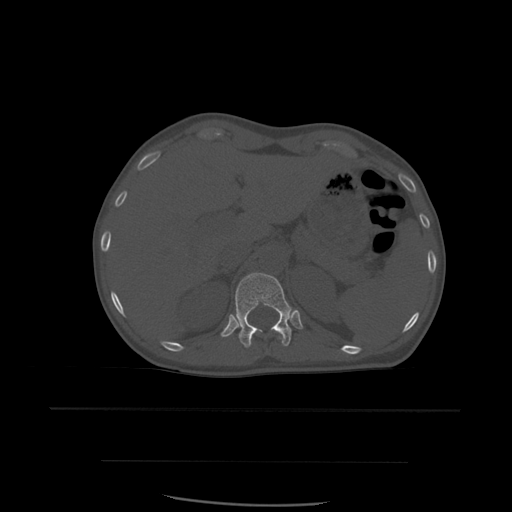
CT including the spine, one axial slice; position 277 of 574 along the scan axis; bone window (W 1800 / L 400 HU); 1.25 mm slice thickness; 512 × 512 image matrix. Patient age 48 years. From the clinical record (not read from this slice): primary cancer: lung; vertebrae with lytic lesions (as recorded): T11.
Outlined on this slice (semi-automatic segmentation, software-assisted and operator-edited):
- T11 vertebra: bounding box <251,337,283,344> (left, top, right, bottom; pixels)
- T12 vertebra: <235,273,292,348>